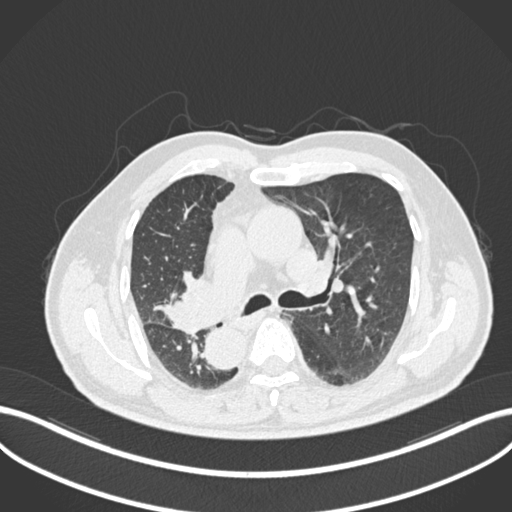
Chest CT, one axial slice. Reconstruction kernel B30f. Lung window (W 1500 / L -600 HU). 1 mm slice thickness. 512 × 512 image matrix. Patient: male, 67 years. From the clinical record (not read from this slice): clinical TNM (as recorded): T2a N0 M0.
Structures marked on this image (bounding box drawn by a radiologist):
- lung tumour (recorded histology: squamous cell carcinoma): bounding box <164,273,222,334> (left, top, right, bottom; pixels)